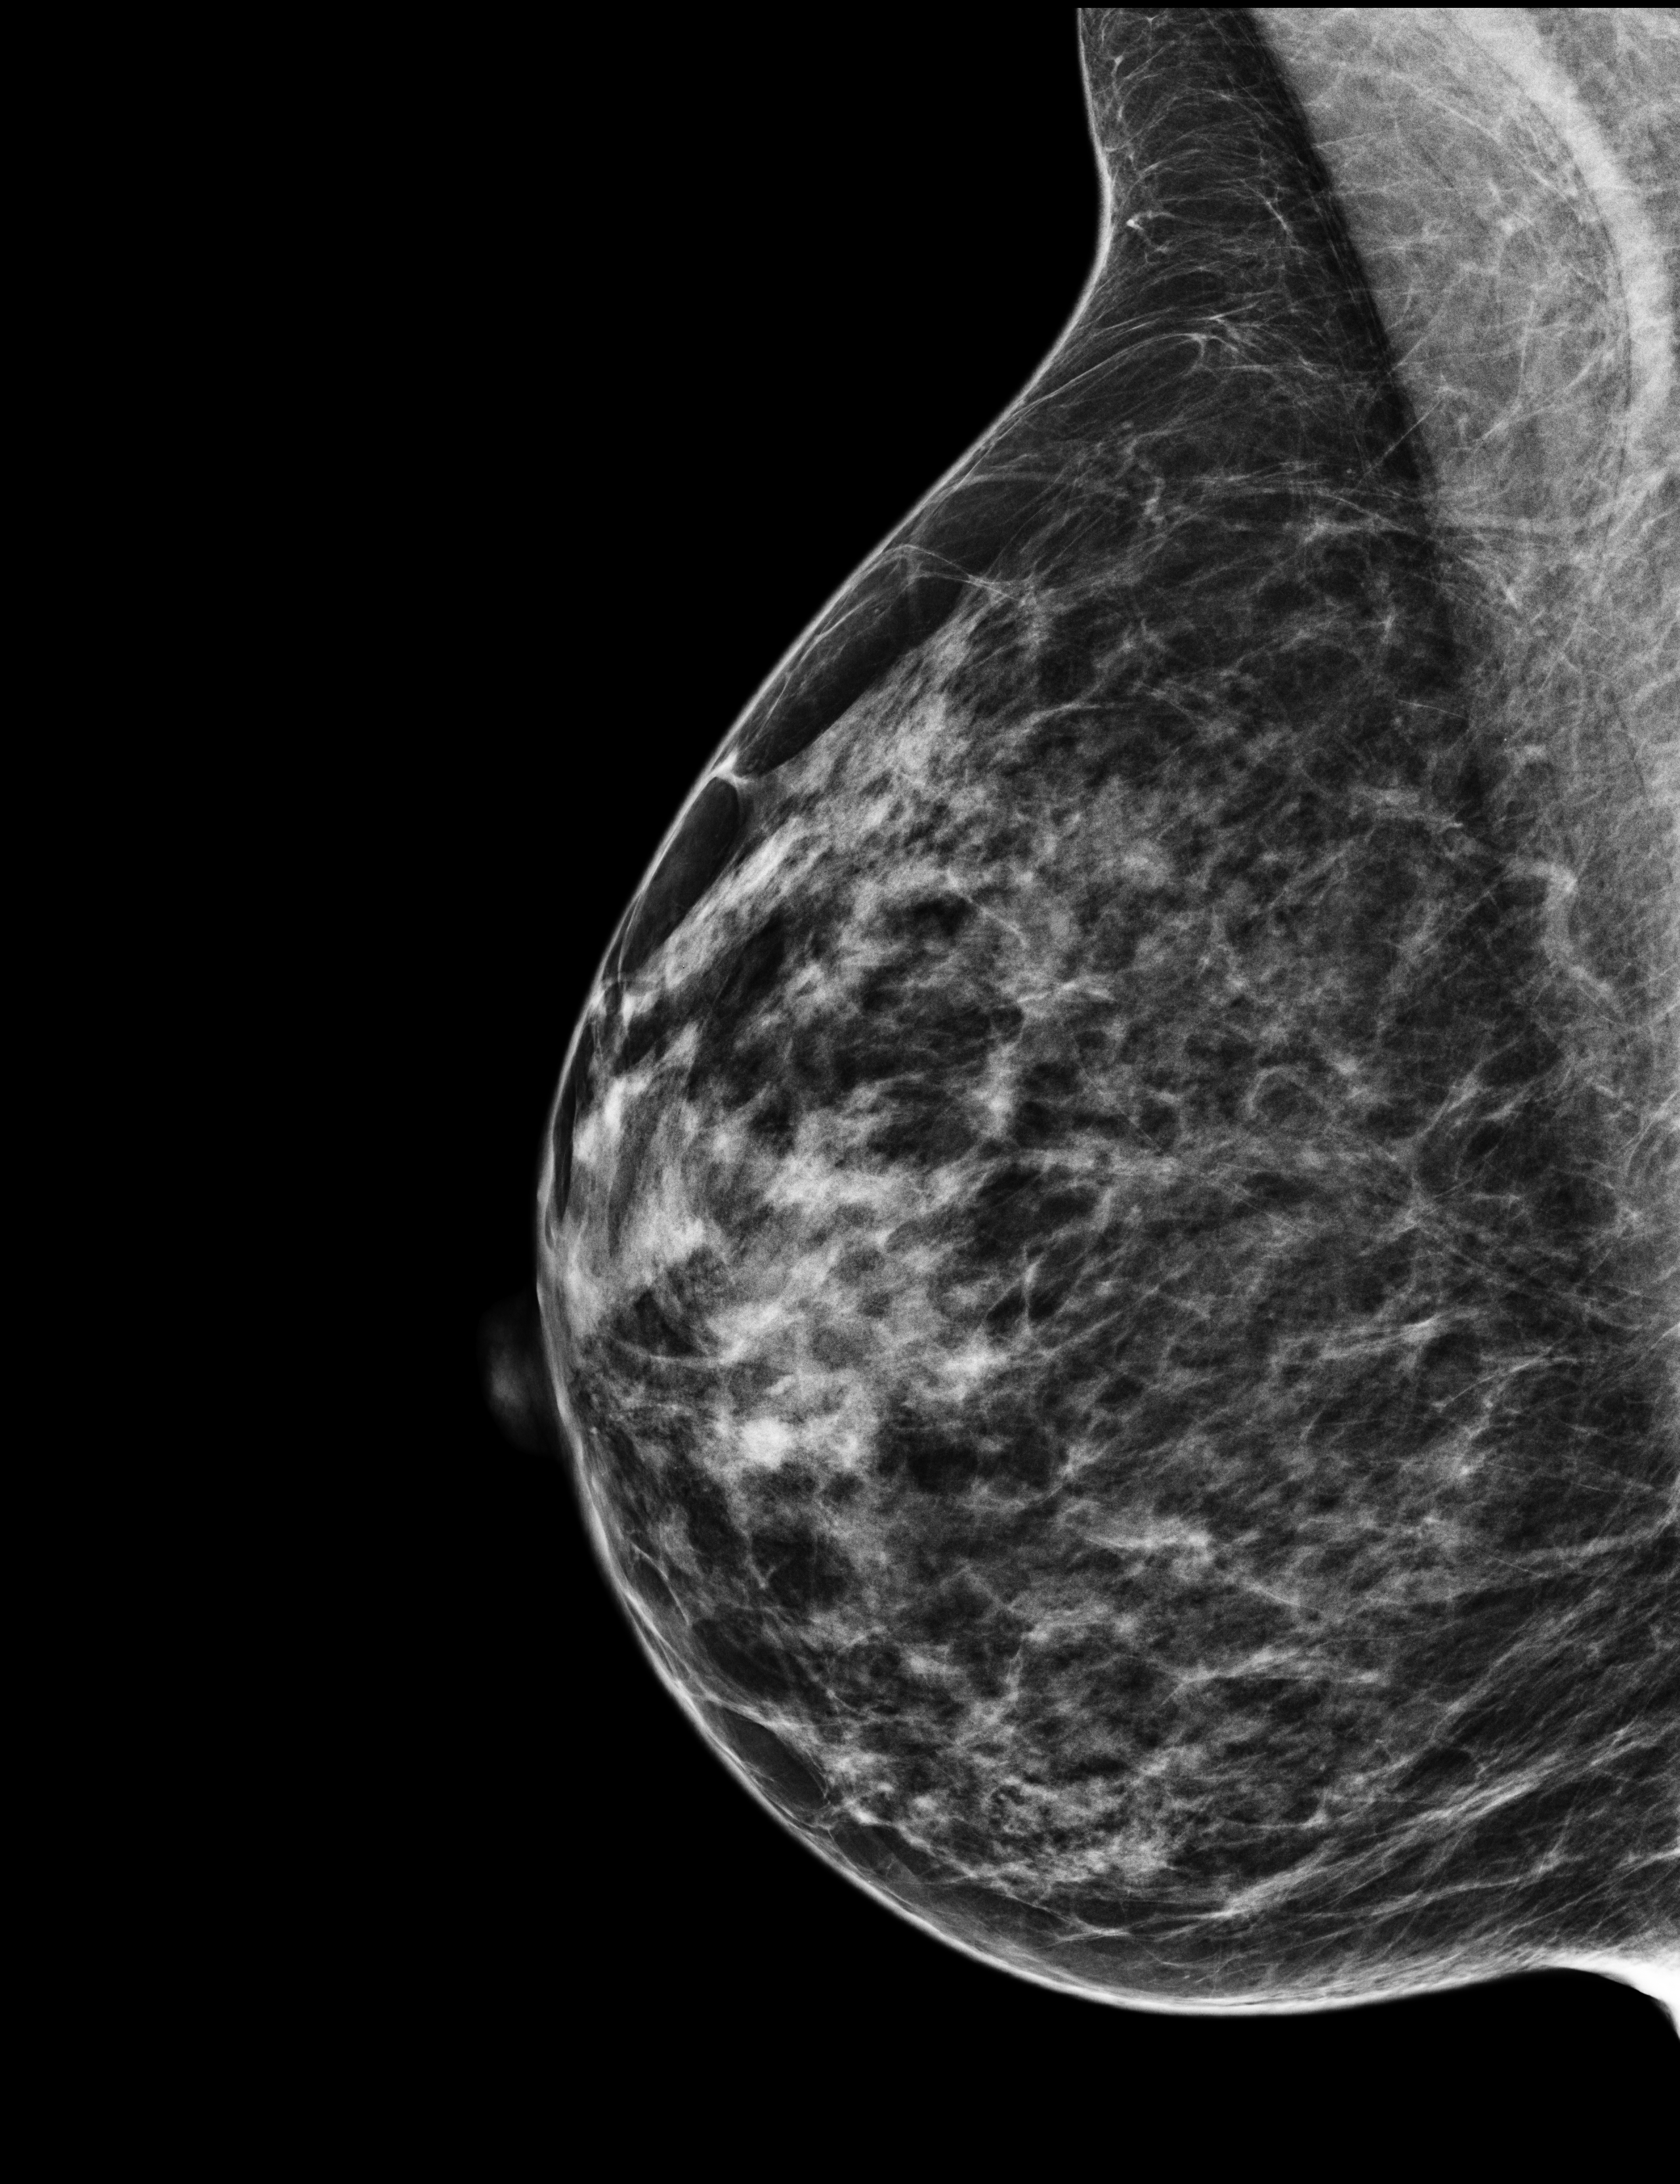
Full-field digital mammogram (FFDM); right breast; medio-lateral oblique projection; annual screening mammography examination; compressed breast thickness 46 mm; system: Selenia Dimensions. Female patient, age 50 years.
BI-RADS breast density category at the screening exam (both breasts, scale 1–4): 3. Final BI-RADS category for the screening round (tomosynthesis exam, both breasts): category 1. Recall: no recall after this screen.